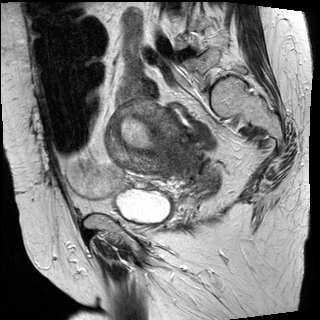
Pelvic MRI for cervical cancer, one sagittal slice; position 20 of 30 along the scan axis; T2-weighted; 1.5 T; TE 89 ms, TR 3810 ms; 4 mm slice thickness; 320 × 320 image matrix, field of view 260 × 260 mm. Patient: female, 62 years.
Structures marked on this image (outlined manually by an expert reader):
- uterus and cervix: bounding box [x1, y1, x2, y2] px = [104, 101, 221, 194]